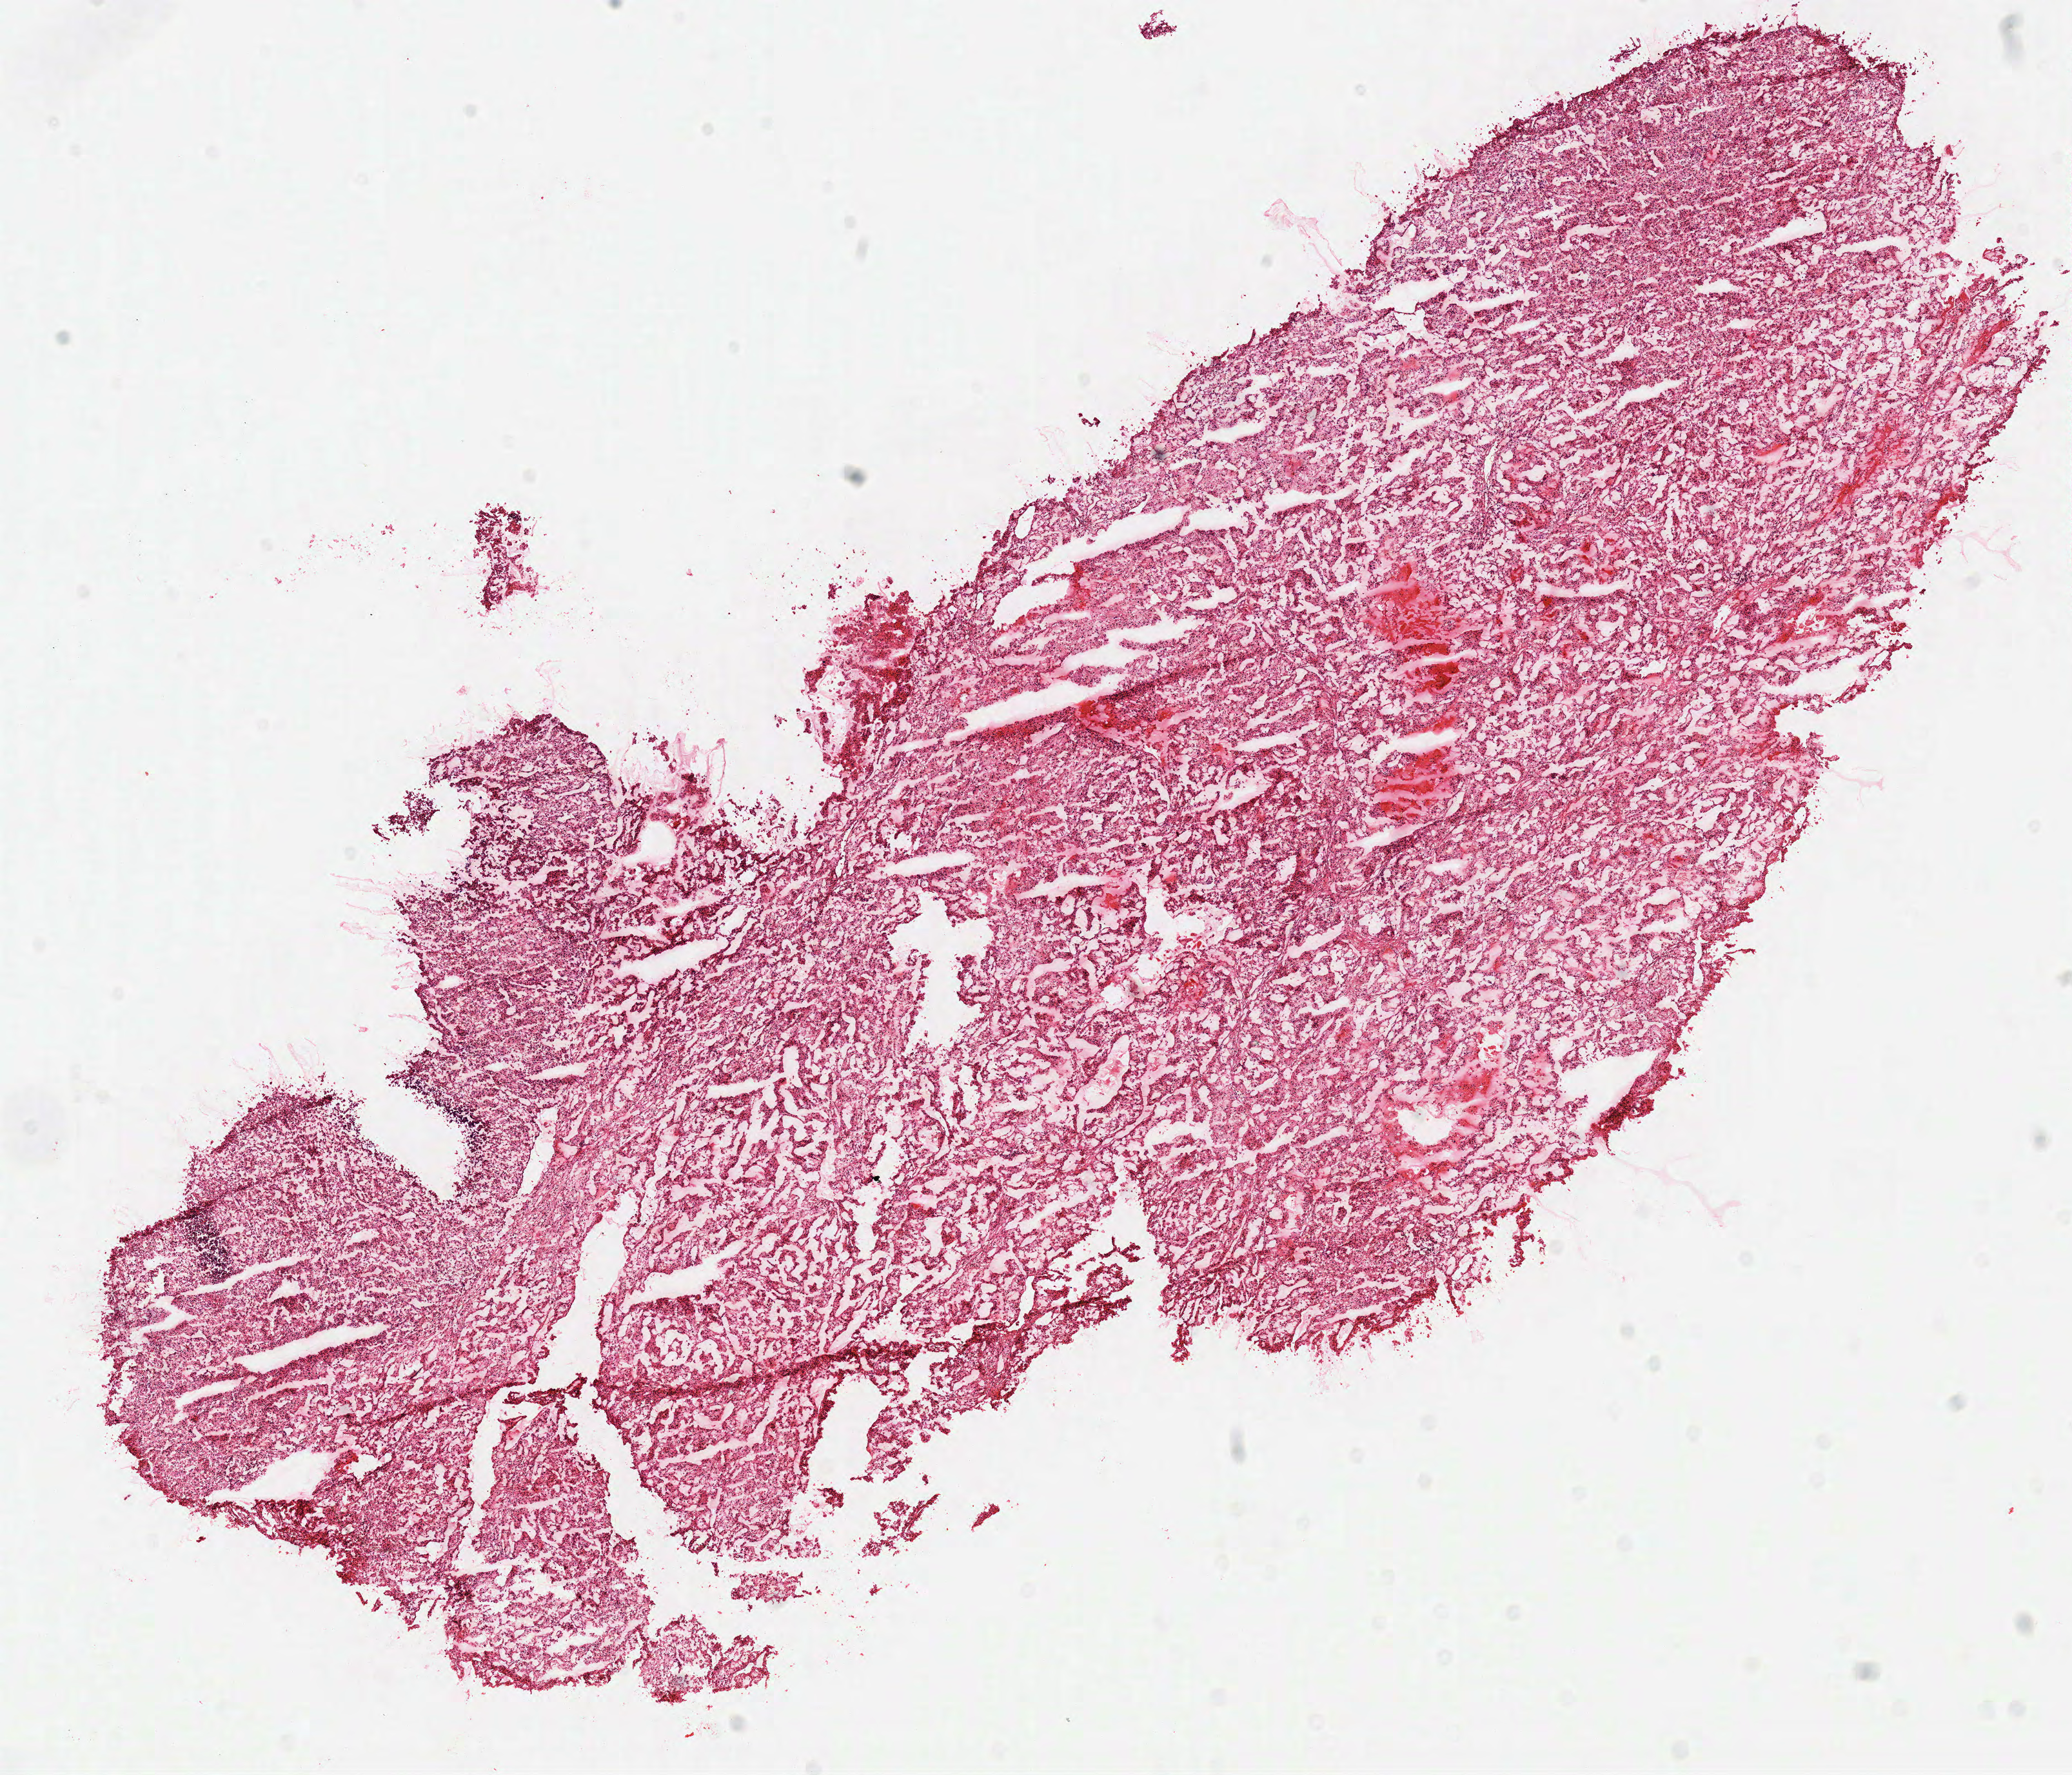
Digitized H&E tissue section (whole slide), shown as a low-resolution overview of the whole scanned area (about 12.7 x 10.8 mm, slide scanned at 40x). Frozen section. Kidney, primary tumour sample. Male, age 60 years at initial diagnosis. Histologic grade: G2 (moderately differentiated). Slide review estimates, as recorded: tumour cells 95%, tumour nuclei 85%, normal cells 0%, stromal cells 5%, necrosis 0%.
AJCC pathologic stage: IV (6th edition). Diagnosis: Clear cell adenocarcinoma, NOS.